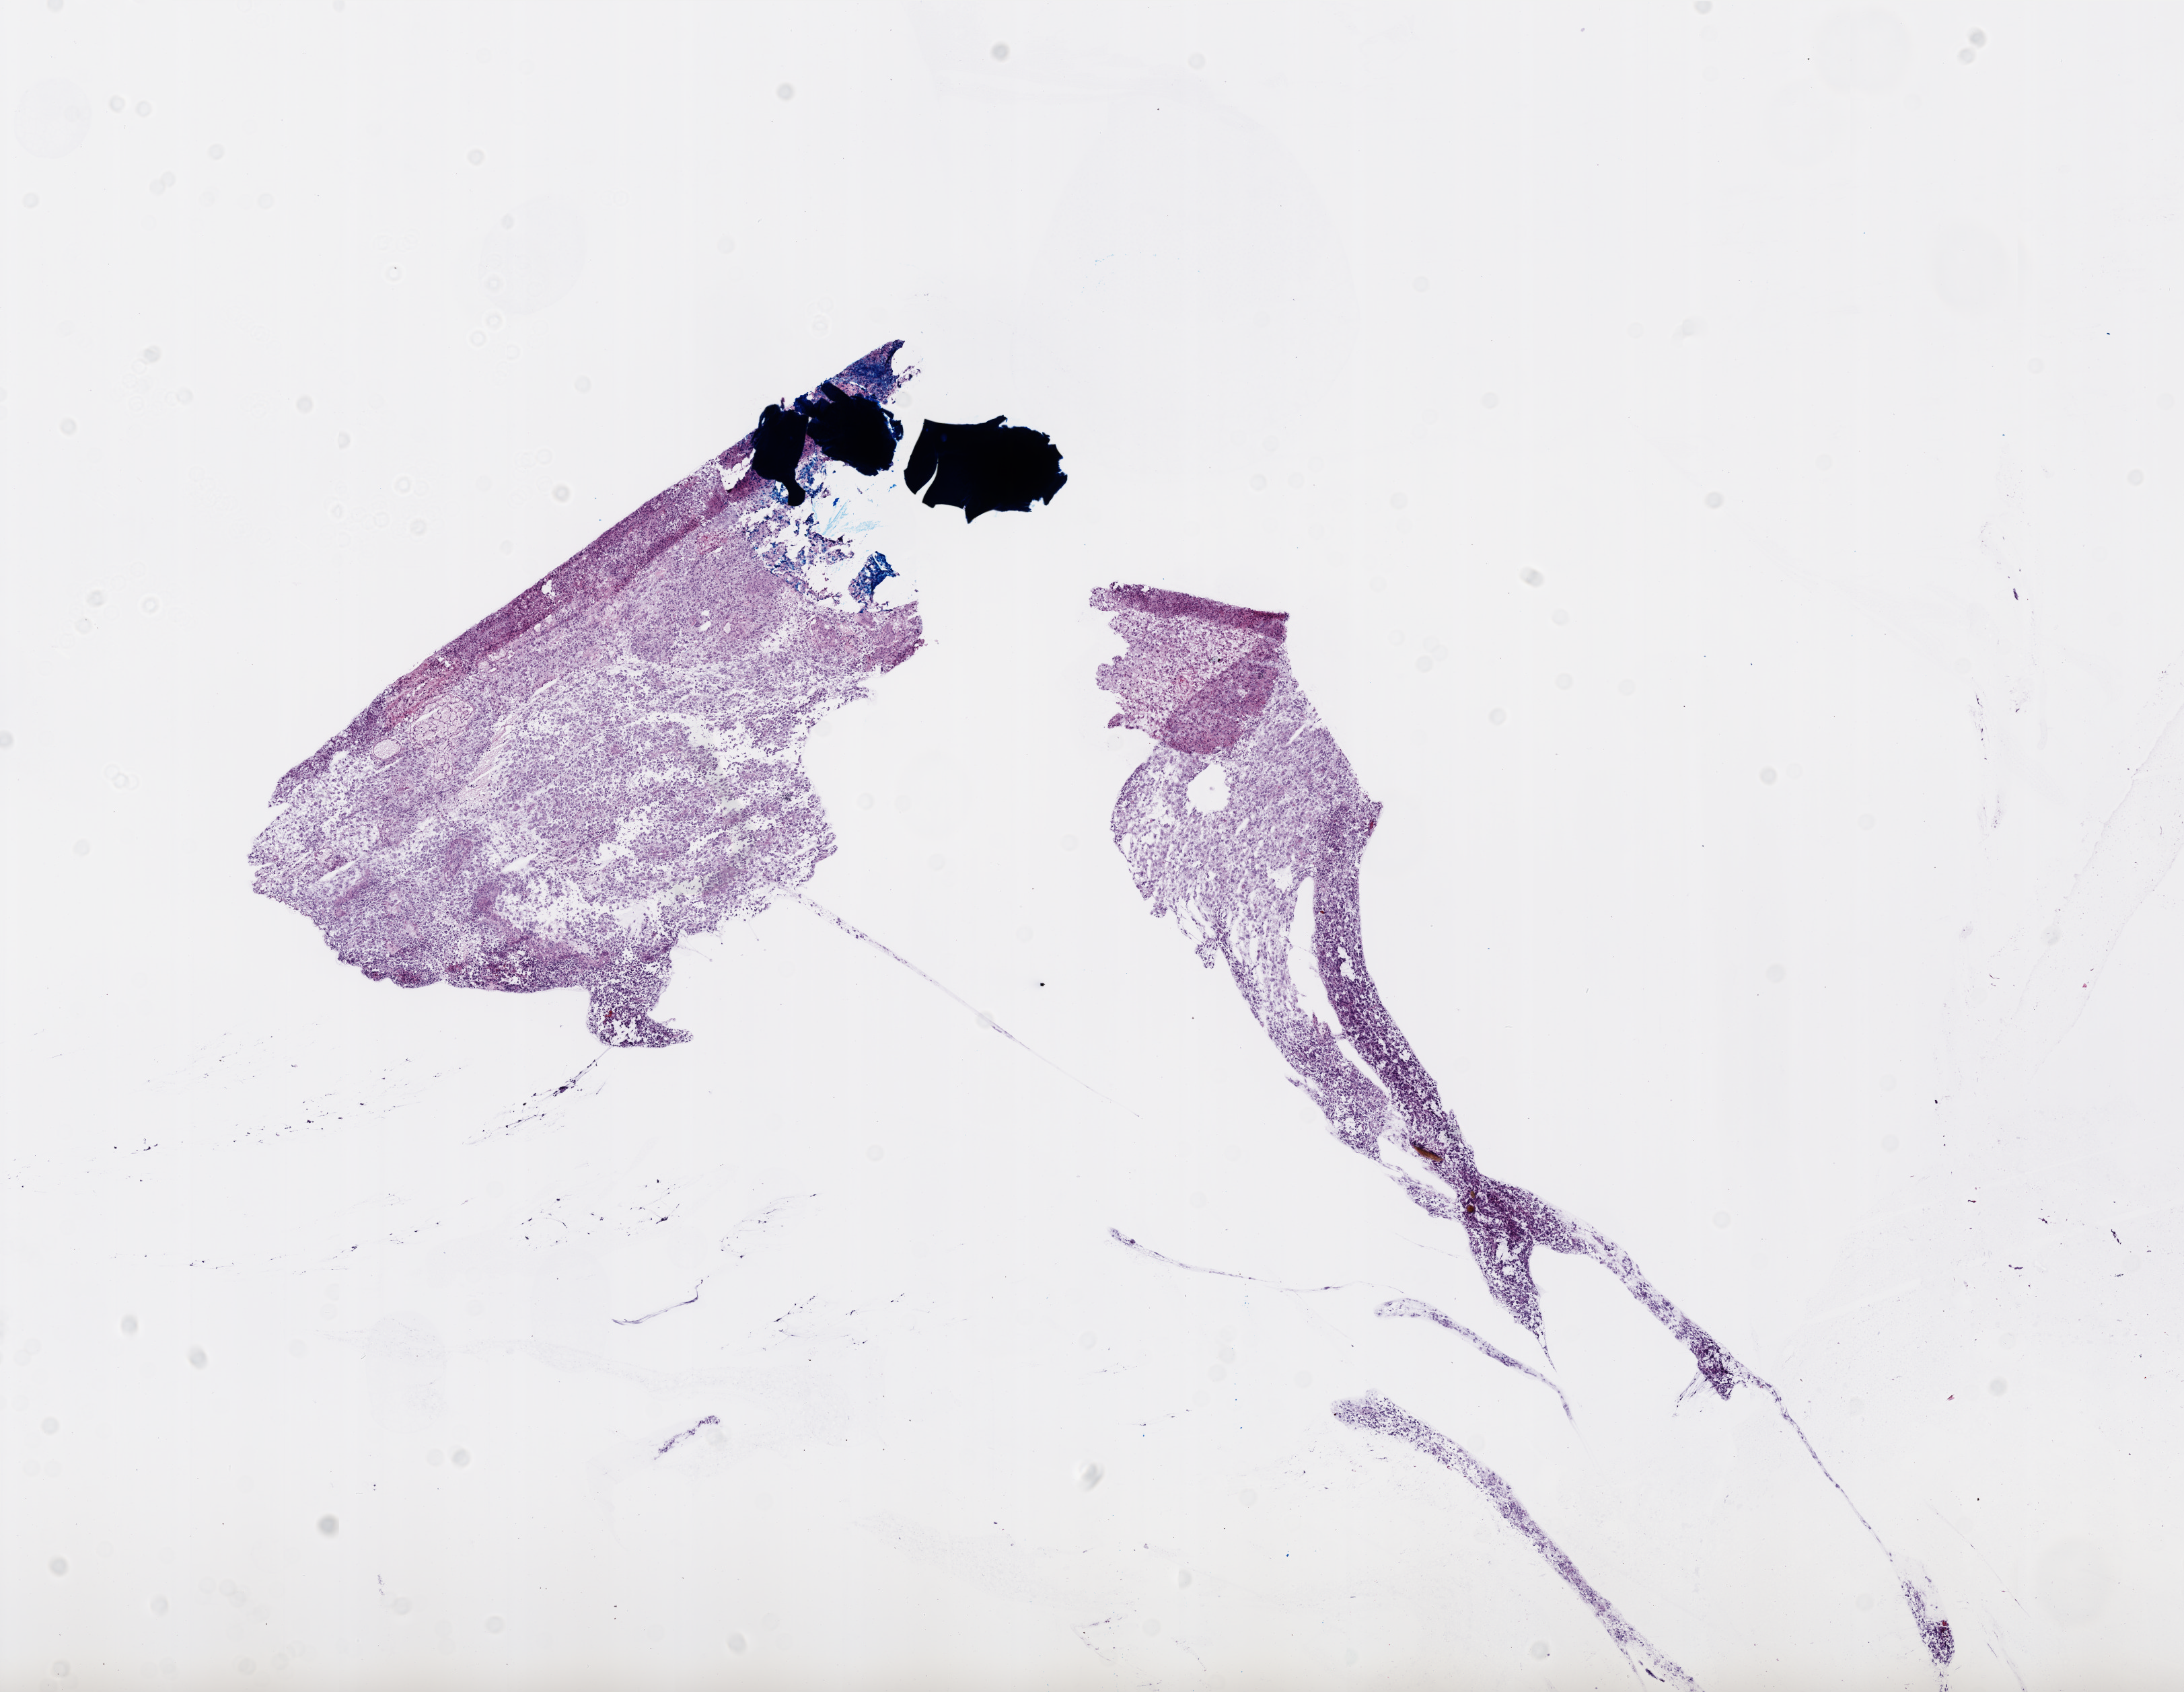
H&E whole-slide image — low-resolution overview of the scanned area, about 13.0 x 10.1 mm; frozen section from the top of the tissue portion; primary tumour sample from the brain. Patient: female, age at initial diagnosis 61 years. Pathologist review of this section (percent, as recorded): tumour cells 100%, tumour nuclei 95%.
Pathologic diagnosis: Glioblastoma.